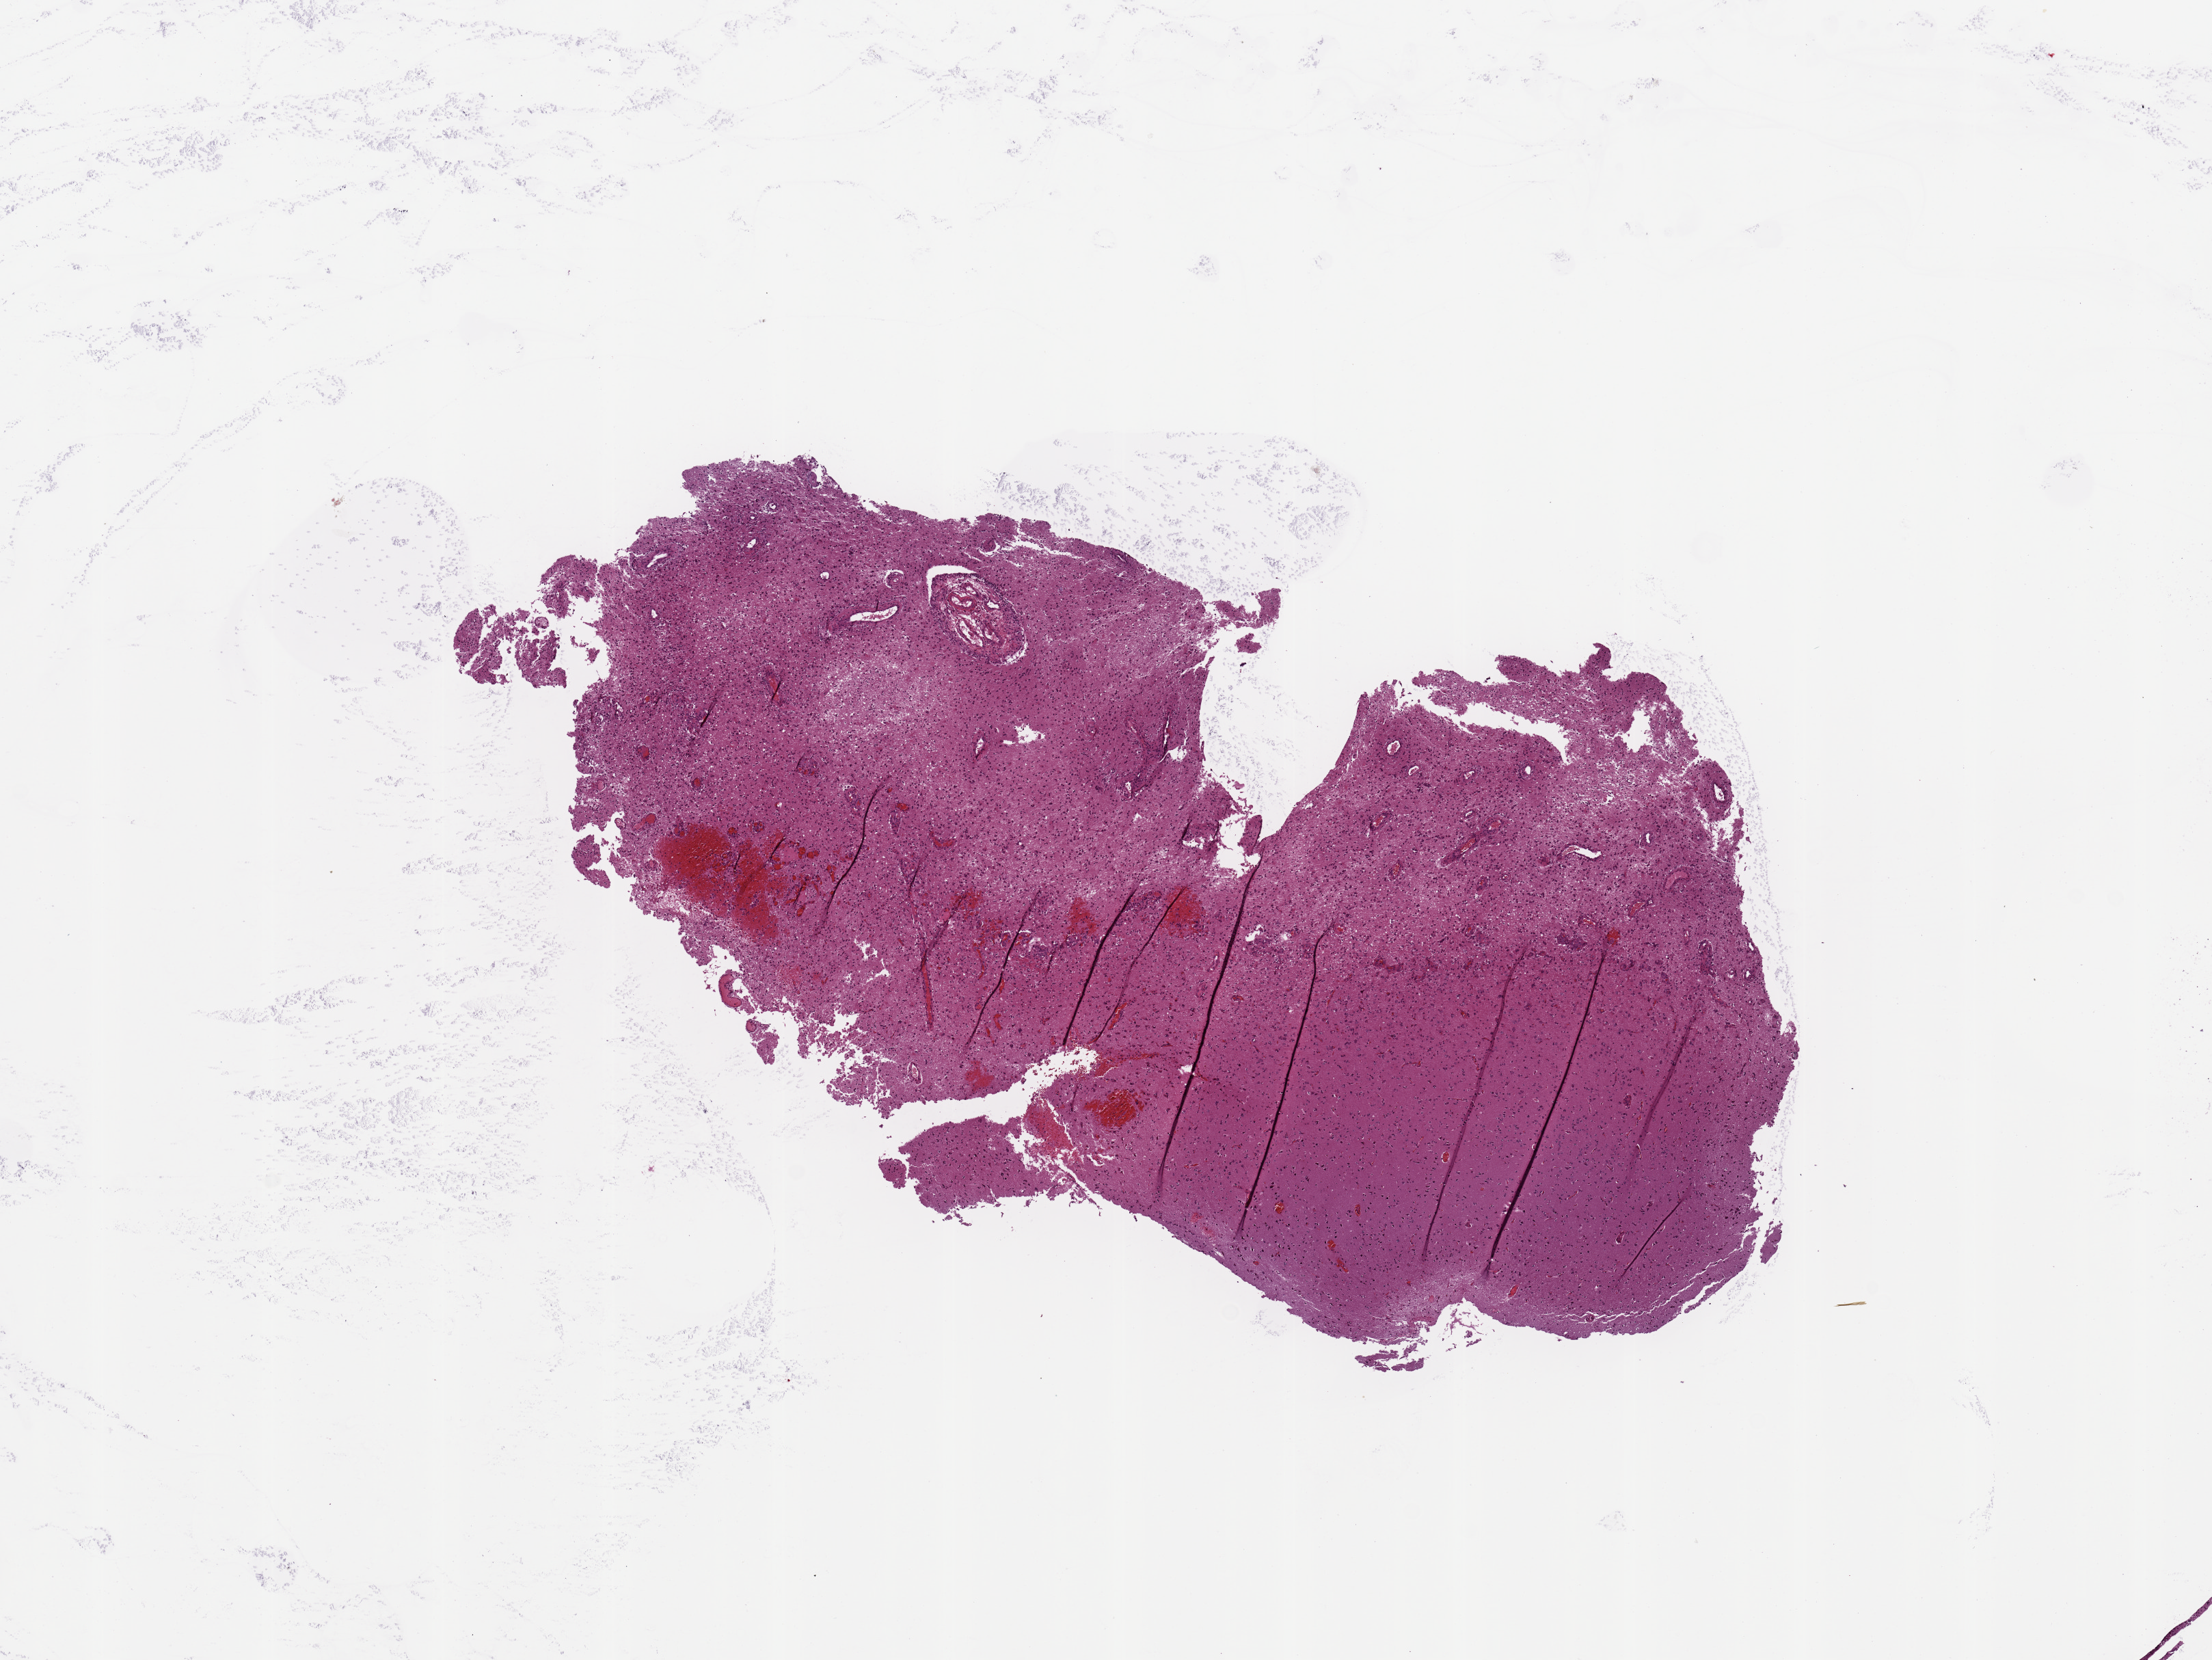
Whole-slide histology image, H&E-stained — whole scanned area (about 12.8 x 9.6 mm) shown as a low-resolution overview. Tumour tissue sample, brain. Male, 53 y/o.
Diagnosis: Glioblastoma.